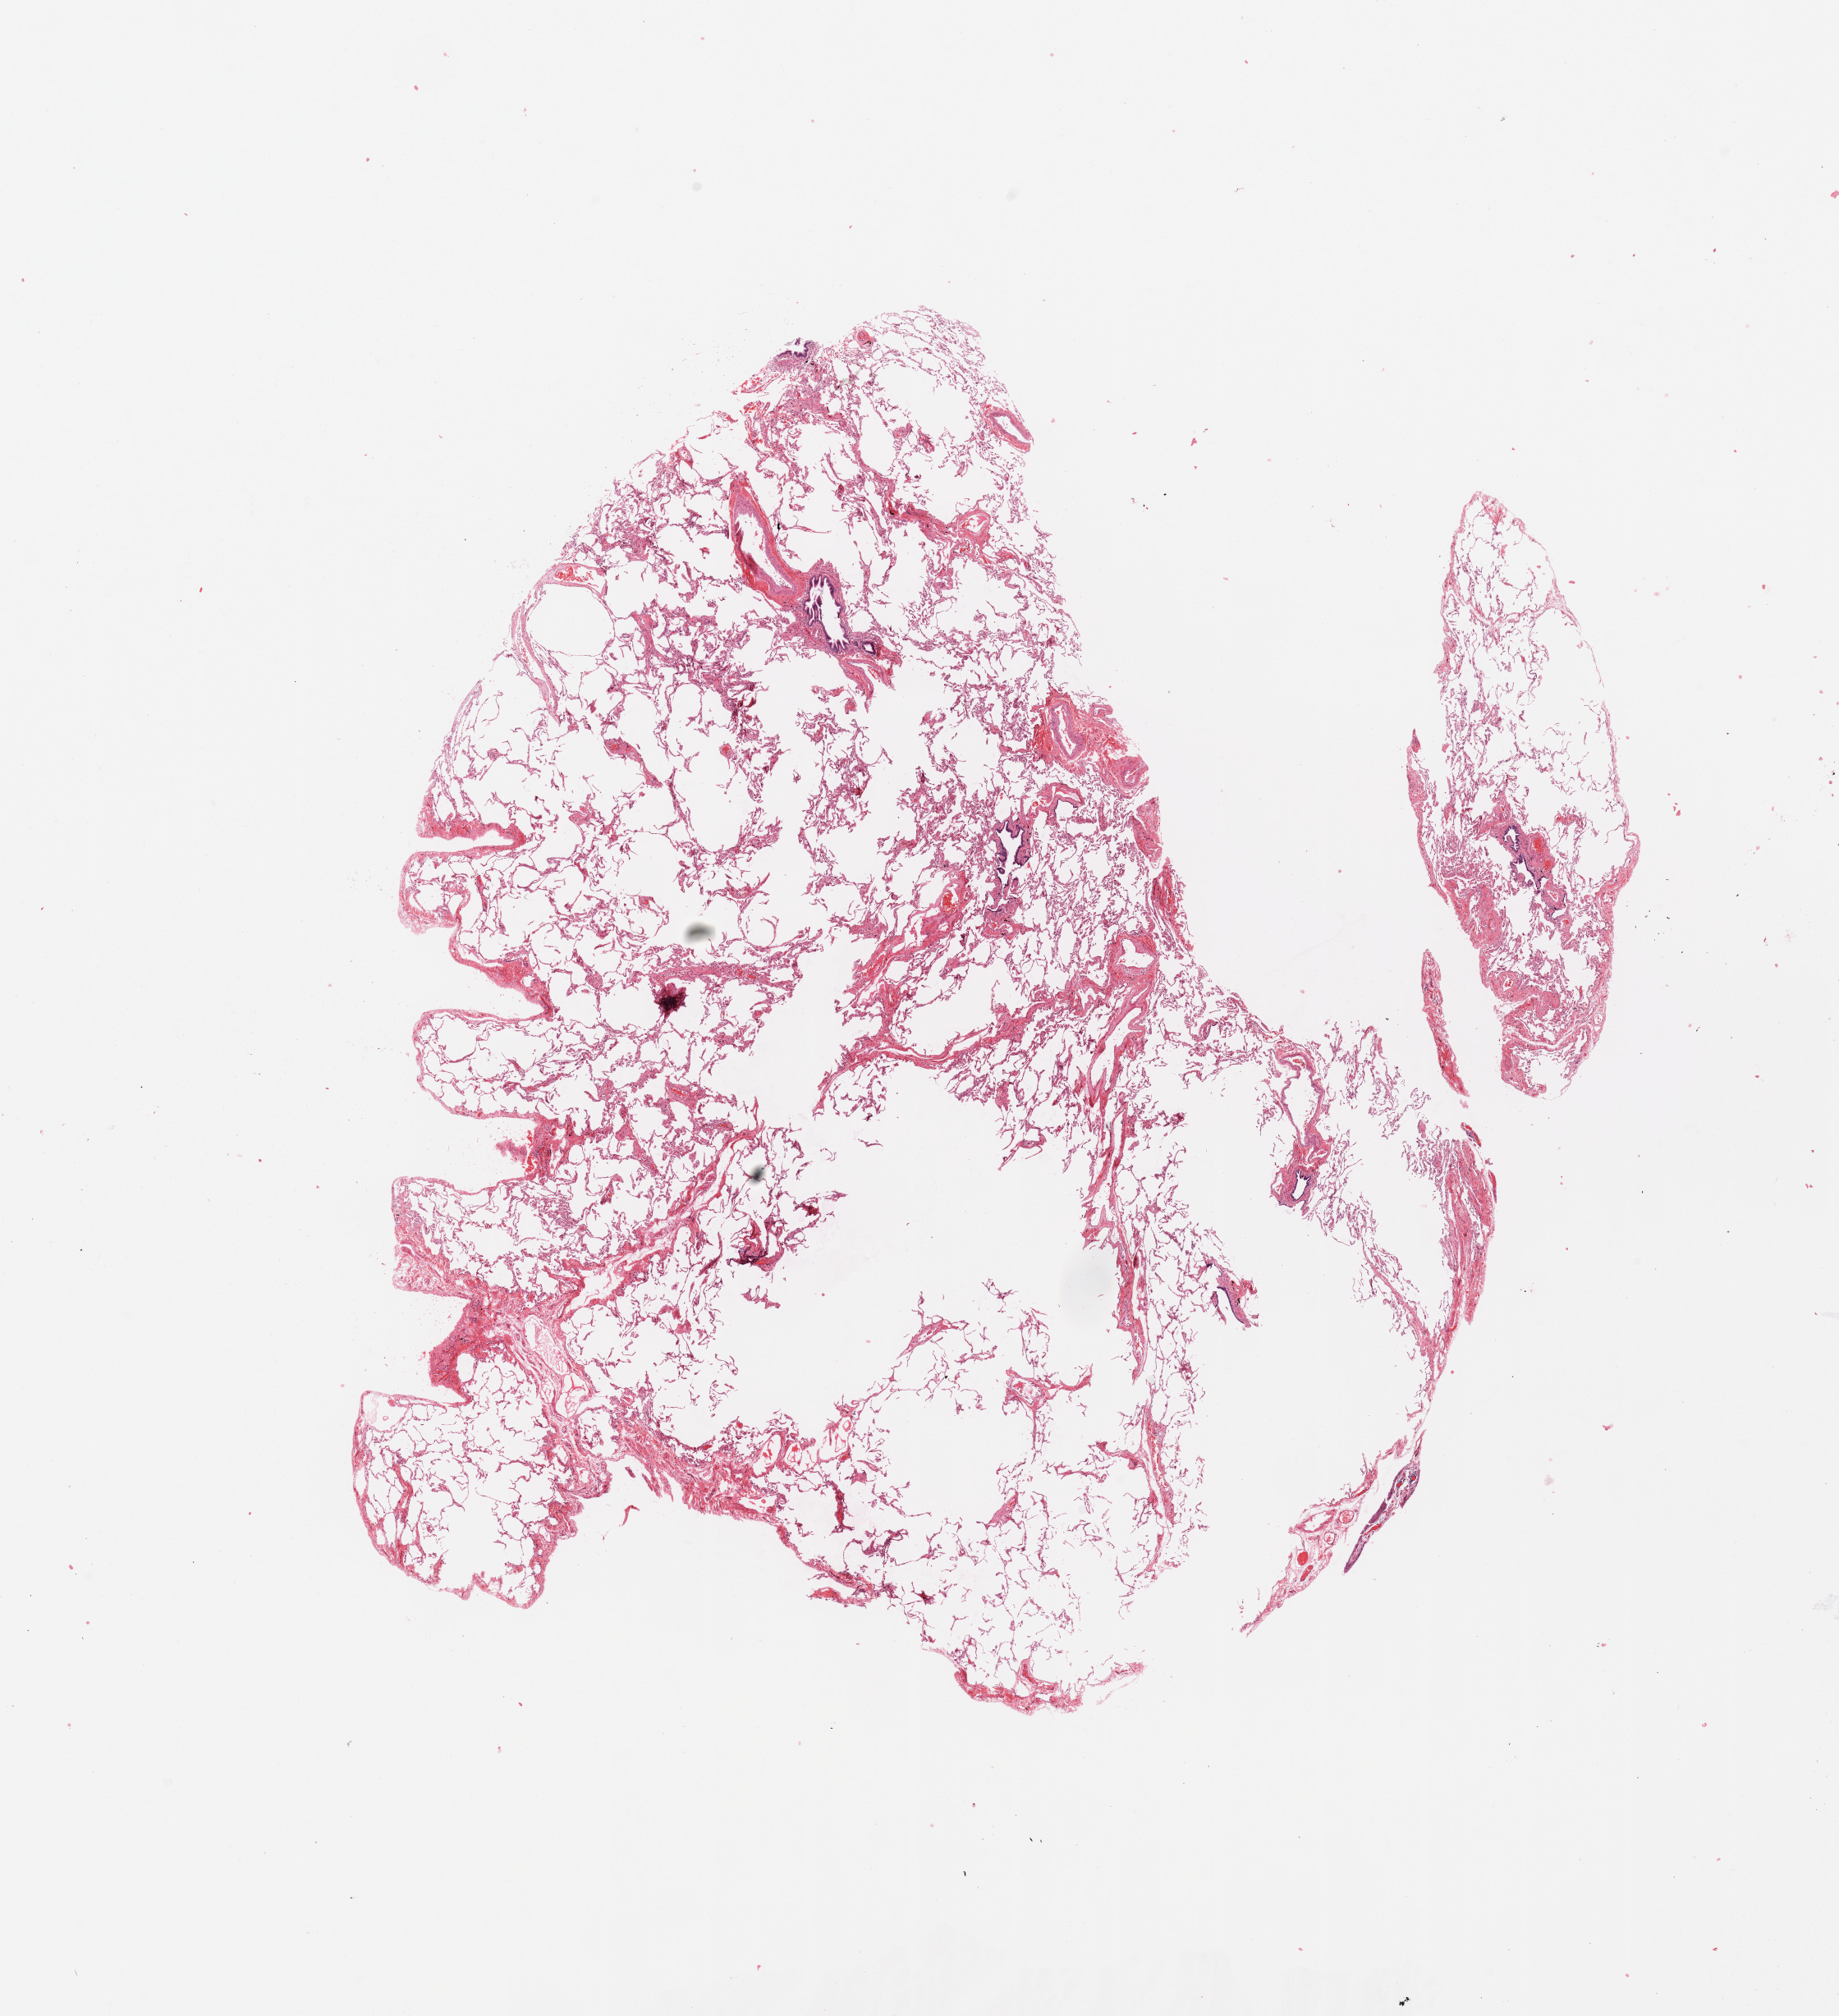
Whole-slide histology image, Hematoxylin and eosin (H&E) stained — low-resolution overview of the scanned area, about 17.7 x 19.4 mm (acquisition: 20x scan); normal (non-tumour) tissue sample, sampled site: lung. 70-year-old male patient.
This section: normal (non-tumour) tissue from the same patient. Patient diagnosis: Adenocarcinoma, NOS.